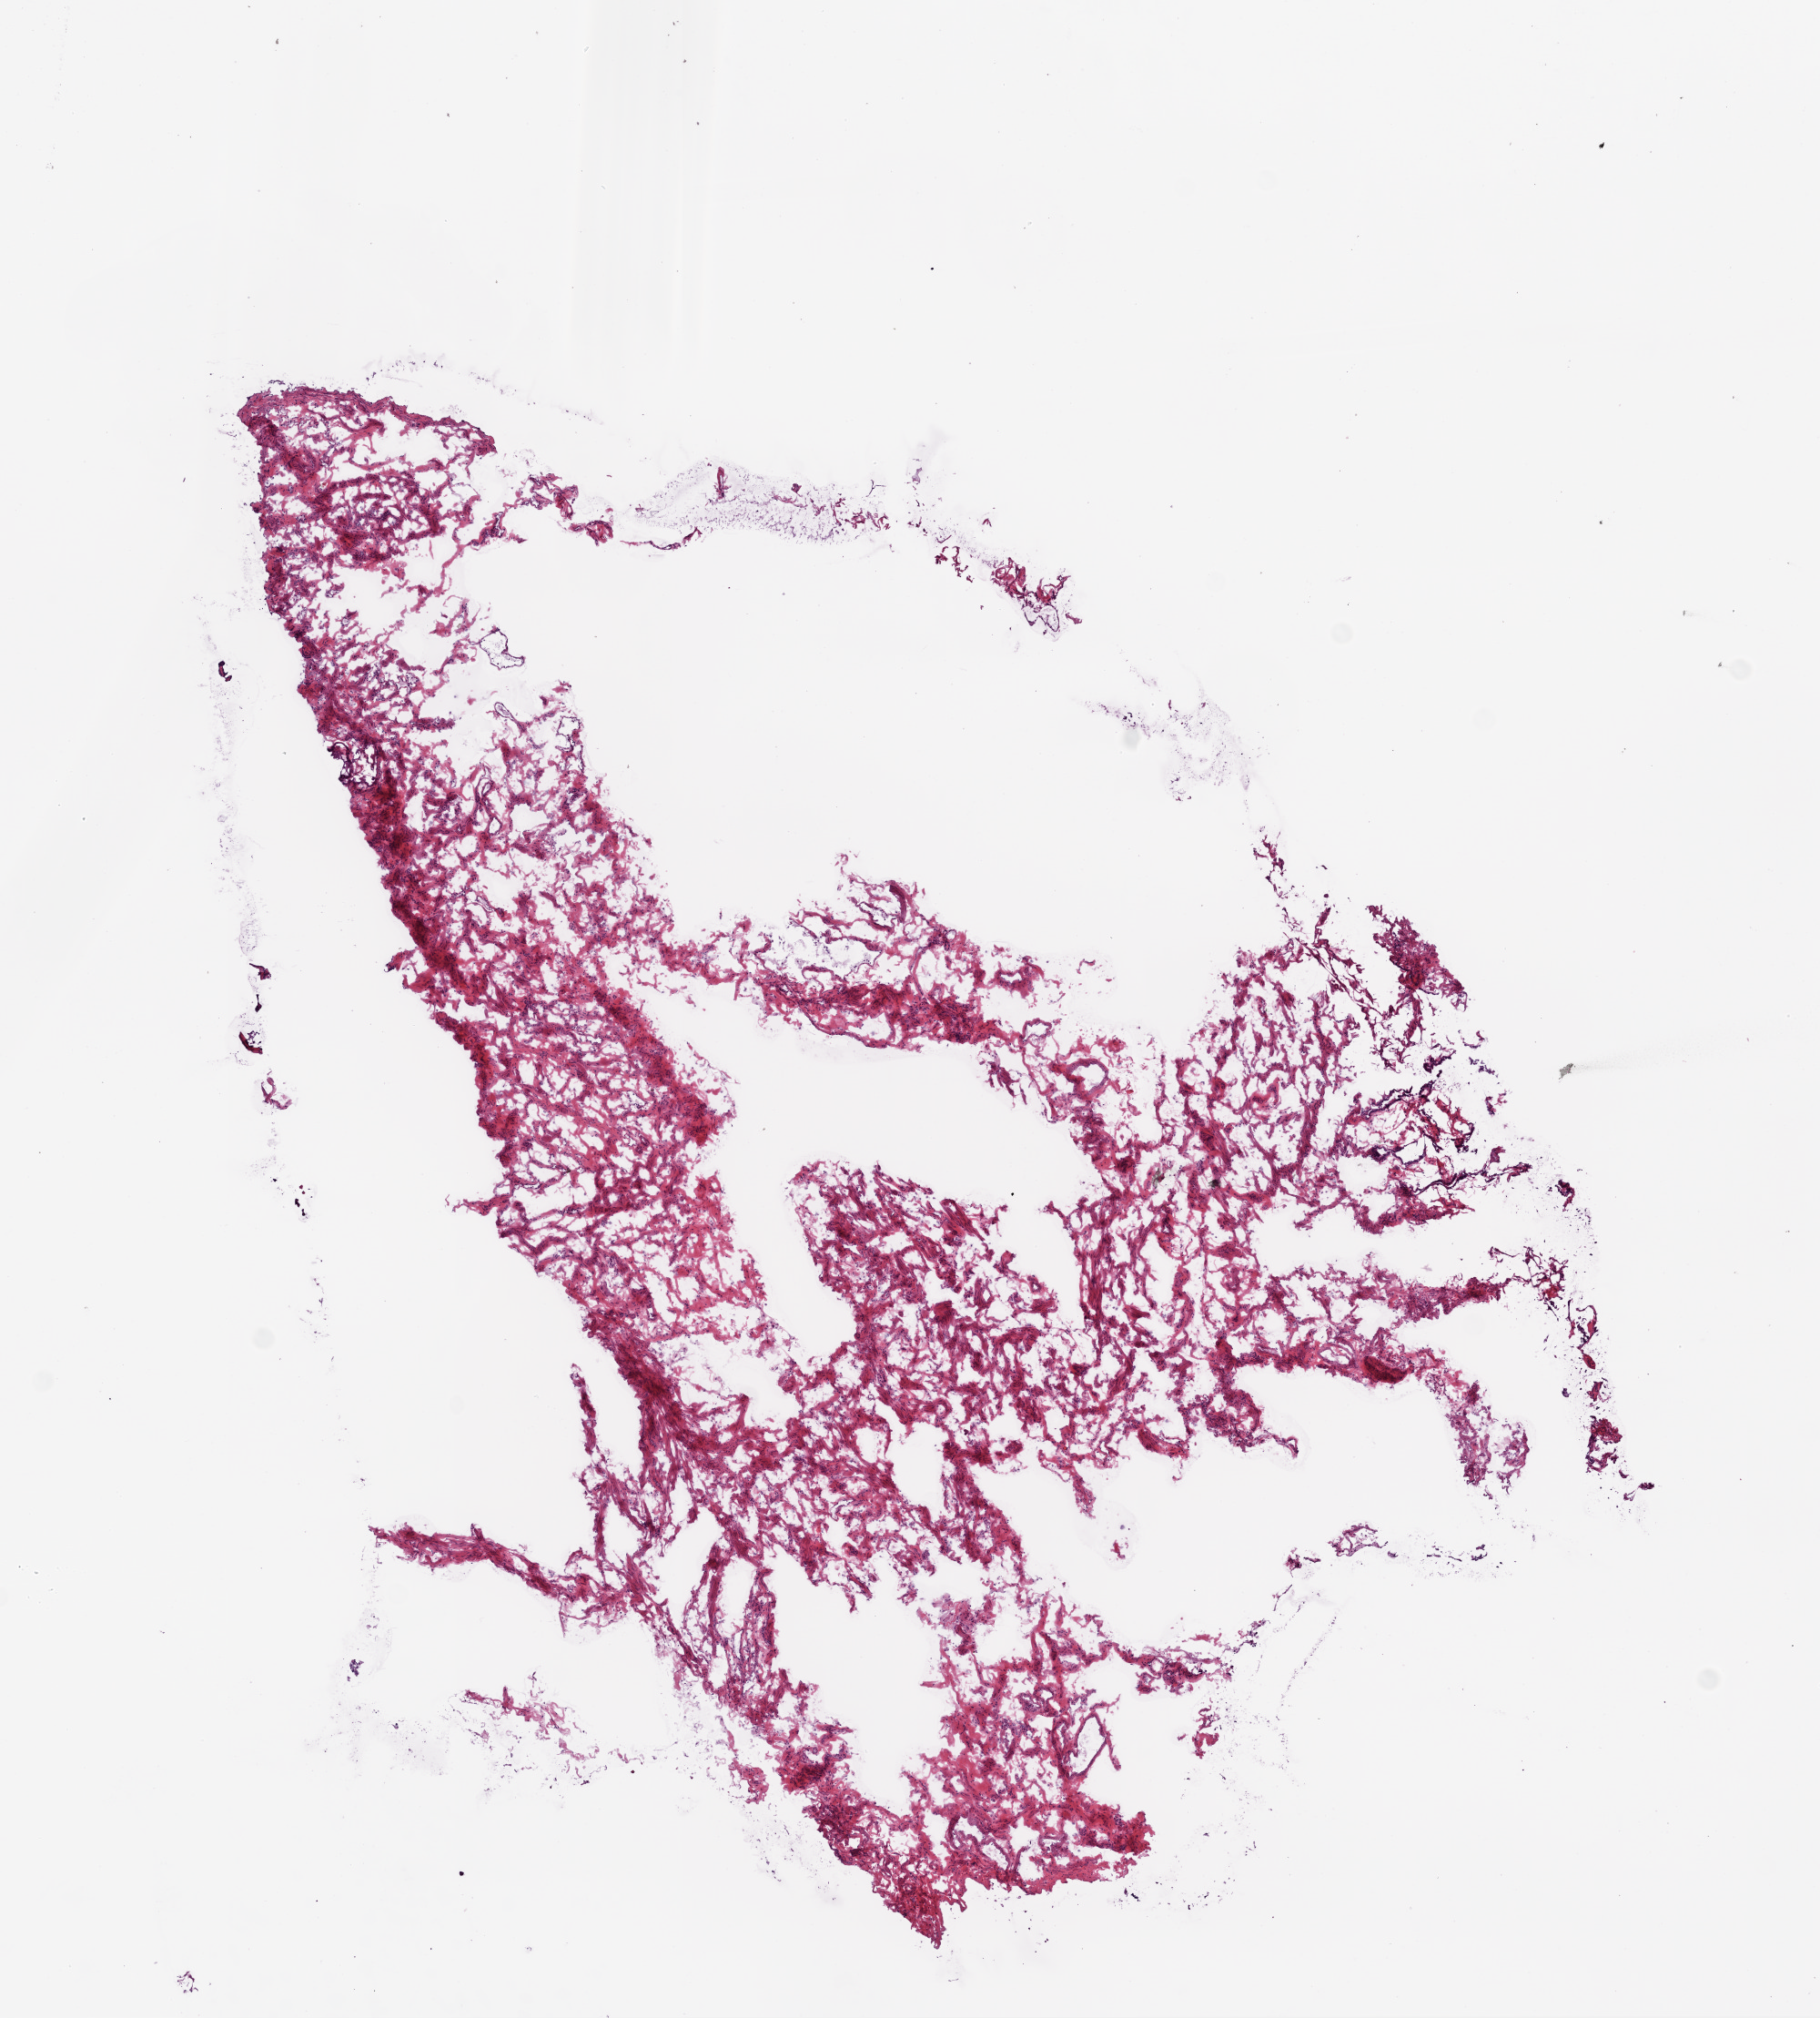
Digitized H&E tissue section (whole slide) — shown as a low-resolution overview of the whole scanned area (about 8.0 x 8.9 mm), frozen section from the bottom of the tissue portion, sample: solid tissue normal (non-tumour tissue), ovary. Female patient; age at initial diagnosis 50 years.
- this section: solid tissue normal (non-tumour) sample from the same patient
- patient diagnosis: Serous cystadenocarcinoma, NOS